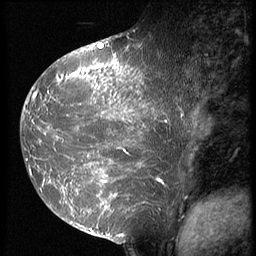
Breast MRI (dynamic contrast-enhanced), one sagittal slice; position 31 of 64 along the scan axis; 3 images stored at this slice position (order not interpretable as contrast timing); 1.5 T; TE 4.2 ms, TR 9 ms; 2.5 mm slice thickness; 256 × 256 image matrix, field of view 180 × 180 mm. Patient: female, 39 years. Case-level facts recorded for this patient, not image findings: setting: breast cancer imaged before/during neoadjuvant chemotherapy; receptor status: HER2-positive.
Annotated regions visible in this slice (semi-automatically segmented with operator editing):
- analysis volume of interest (the breast-tissue region the enhancement analysis was run in; not a lesion): box from (x=23, y=47) to (x=179, y=239) px
- tumour enhancement mask (voxels above the 140 % enhancement threshold inside the analysis volume of interest): (x=23, y=47)–(x=169, y=217)